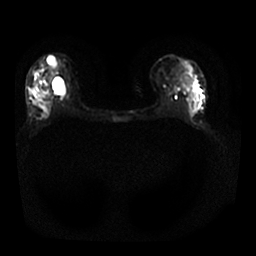
Breast MRI, one axial slice. Slice 12 of 25 in the series (ordered by position). Diffusion-weighted series; image 2 of 4 stored at this slice position (different b-values; order by instance number). 1.5 T. 4 mm slice thickness. 256 × 256 image matrix. Female patient.
Annotated regions visible in this slice (outlined manually by an expert reader):
- tumour on diffusion-weighted imaging: bounding box <44,94,52,119> (left, top, right, bottom; pixels)